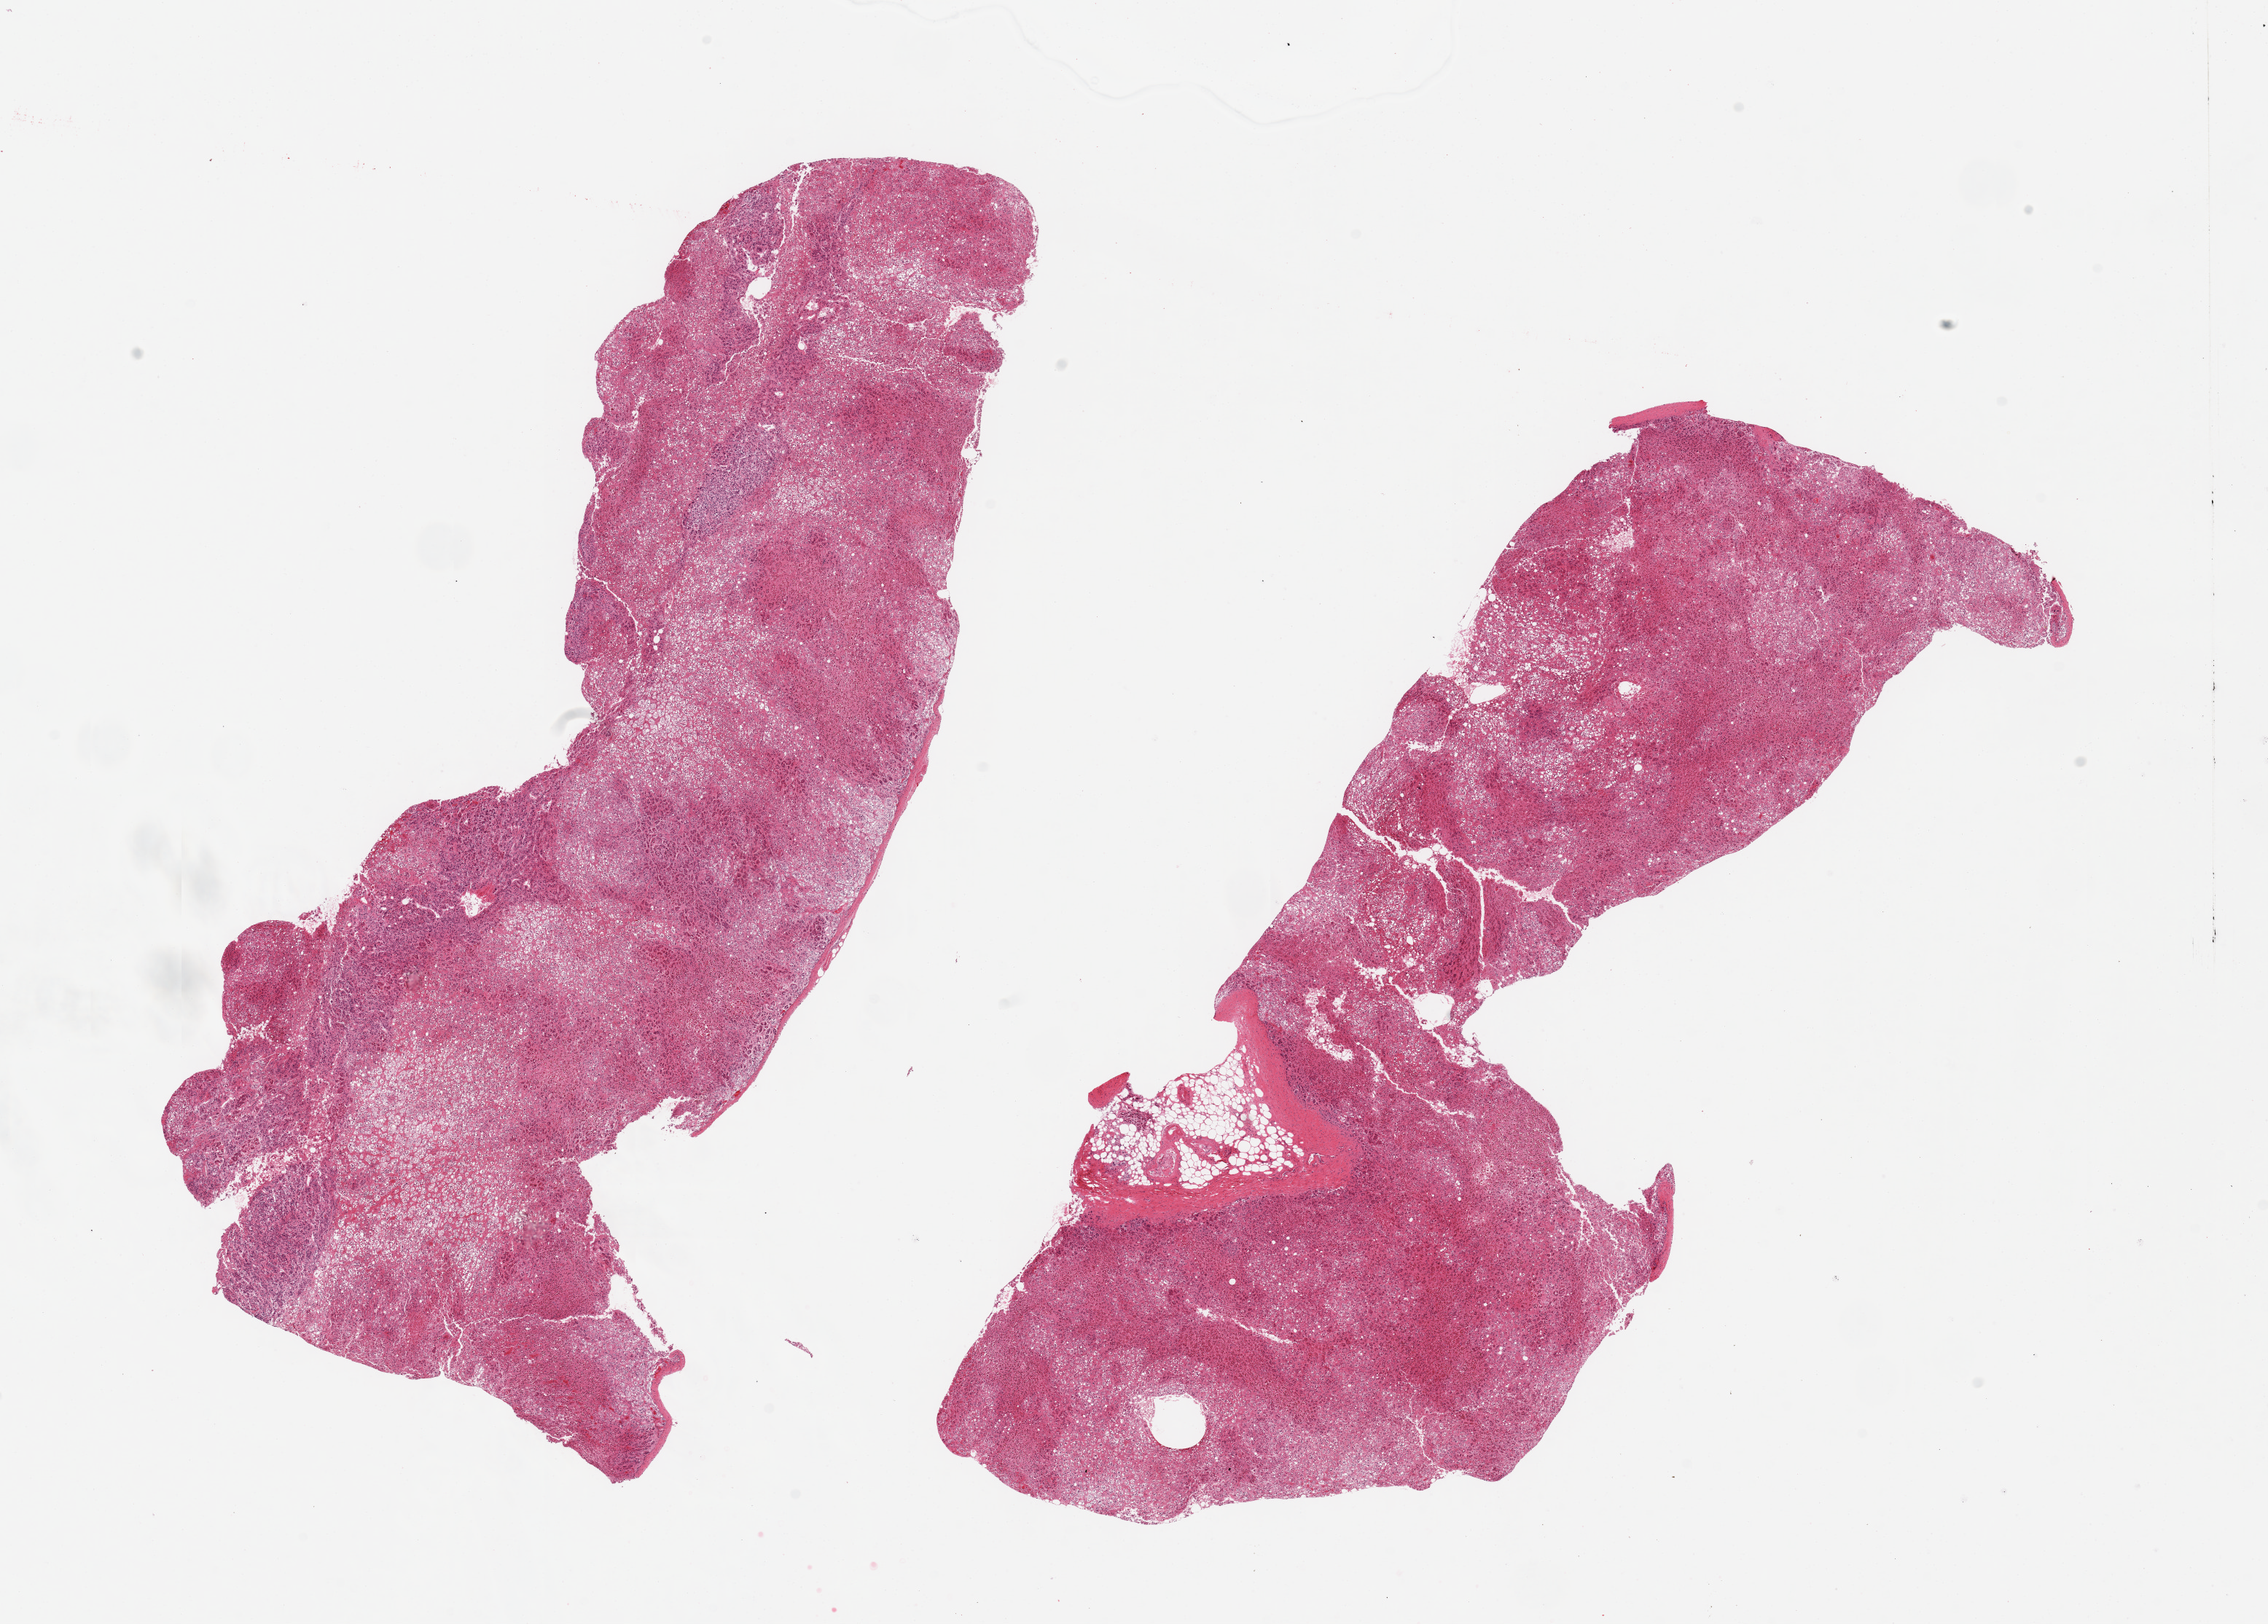
Whole-slide image, haematoxylin and eosin stain — shown as a low-resolution overview of the whole scanned area (about 24.6 x 17.6 mm), PAXgene-fixed, paraffin-embedded tissue, section of adrenal gland (target tissue), donor tissue sample.
* pathologist's review note for this sample: 2 pieces; moderate to severe autolysis